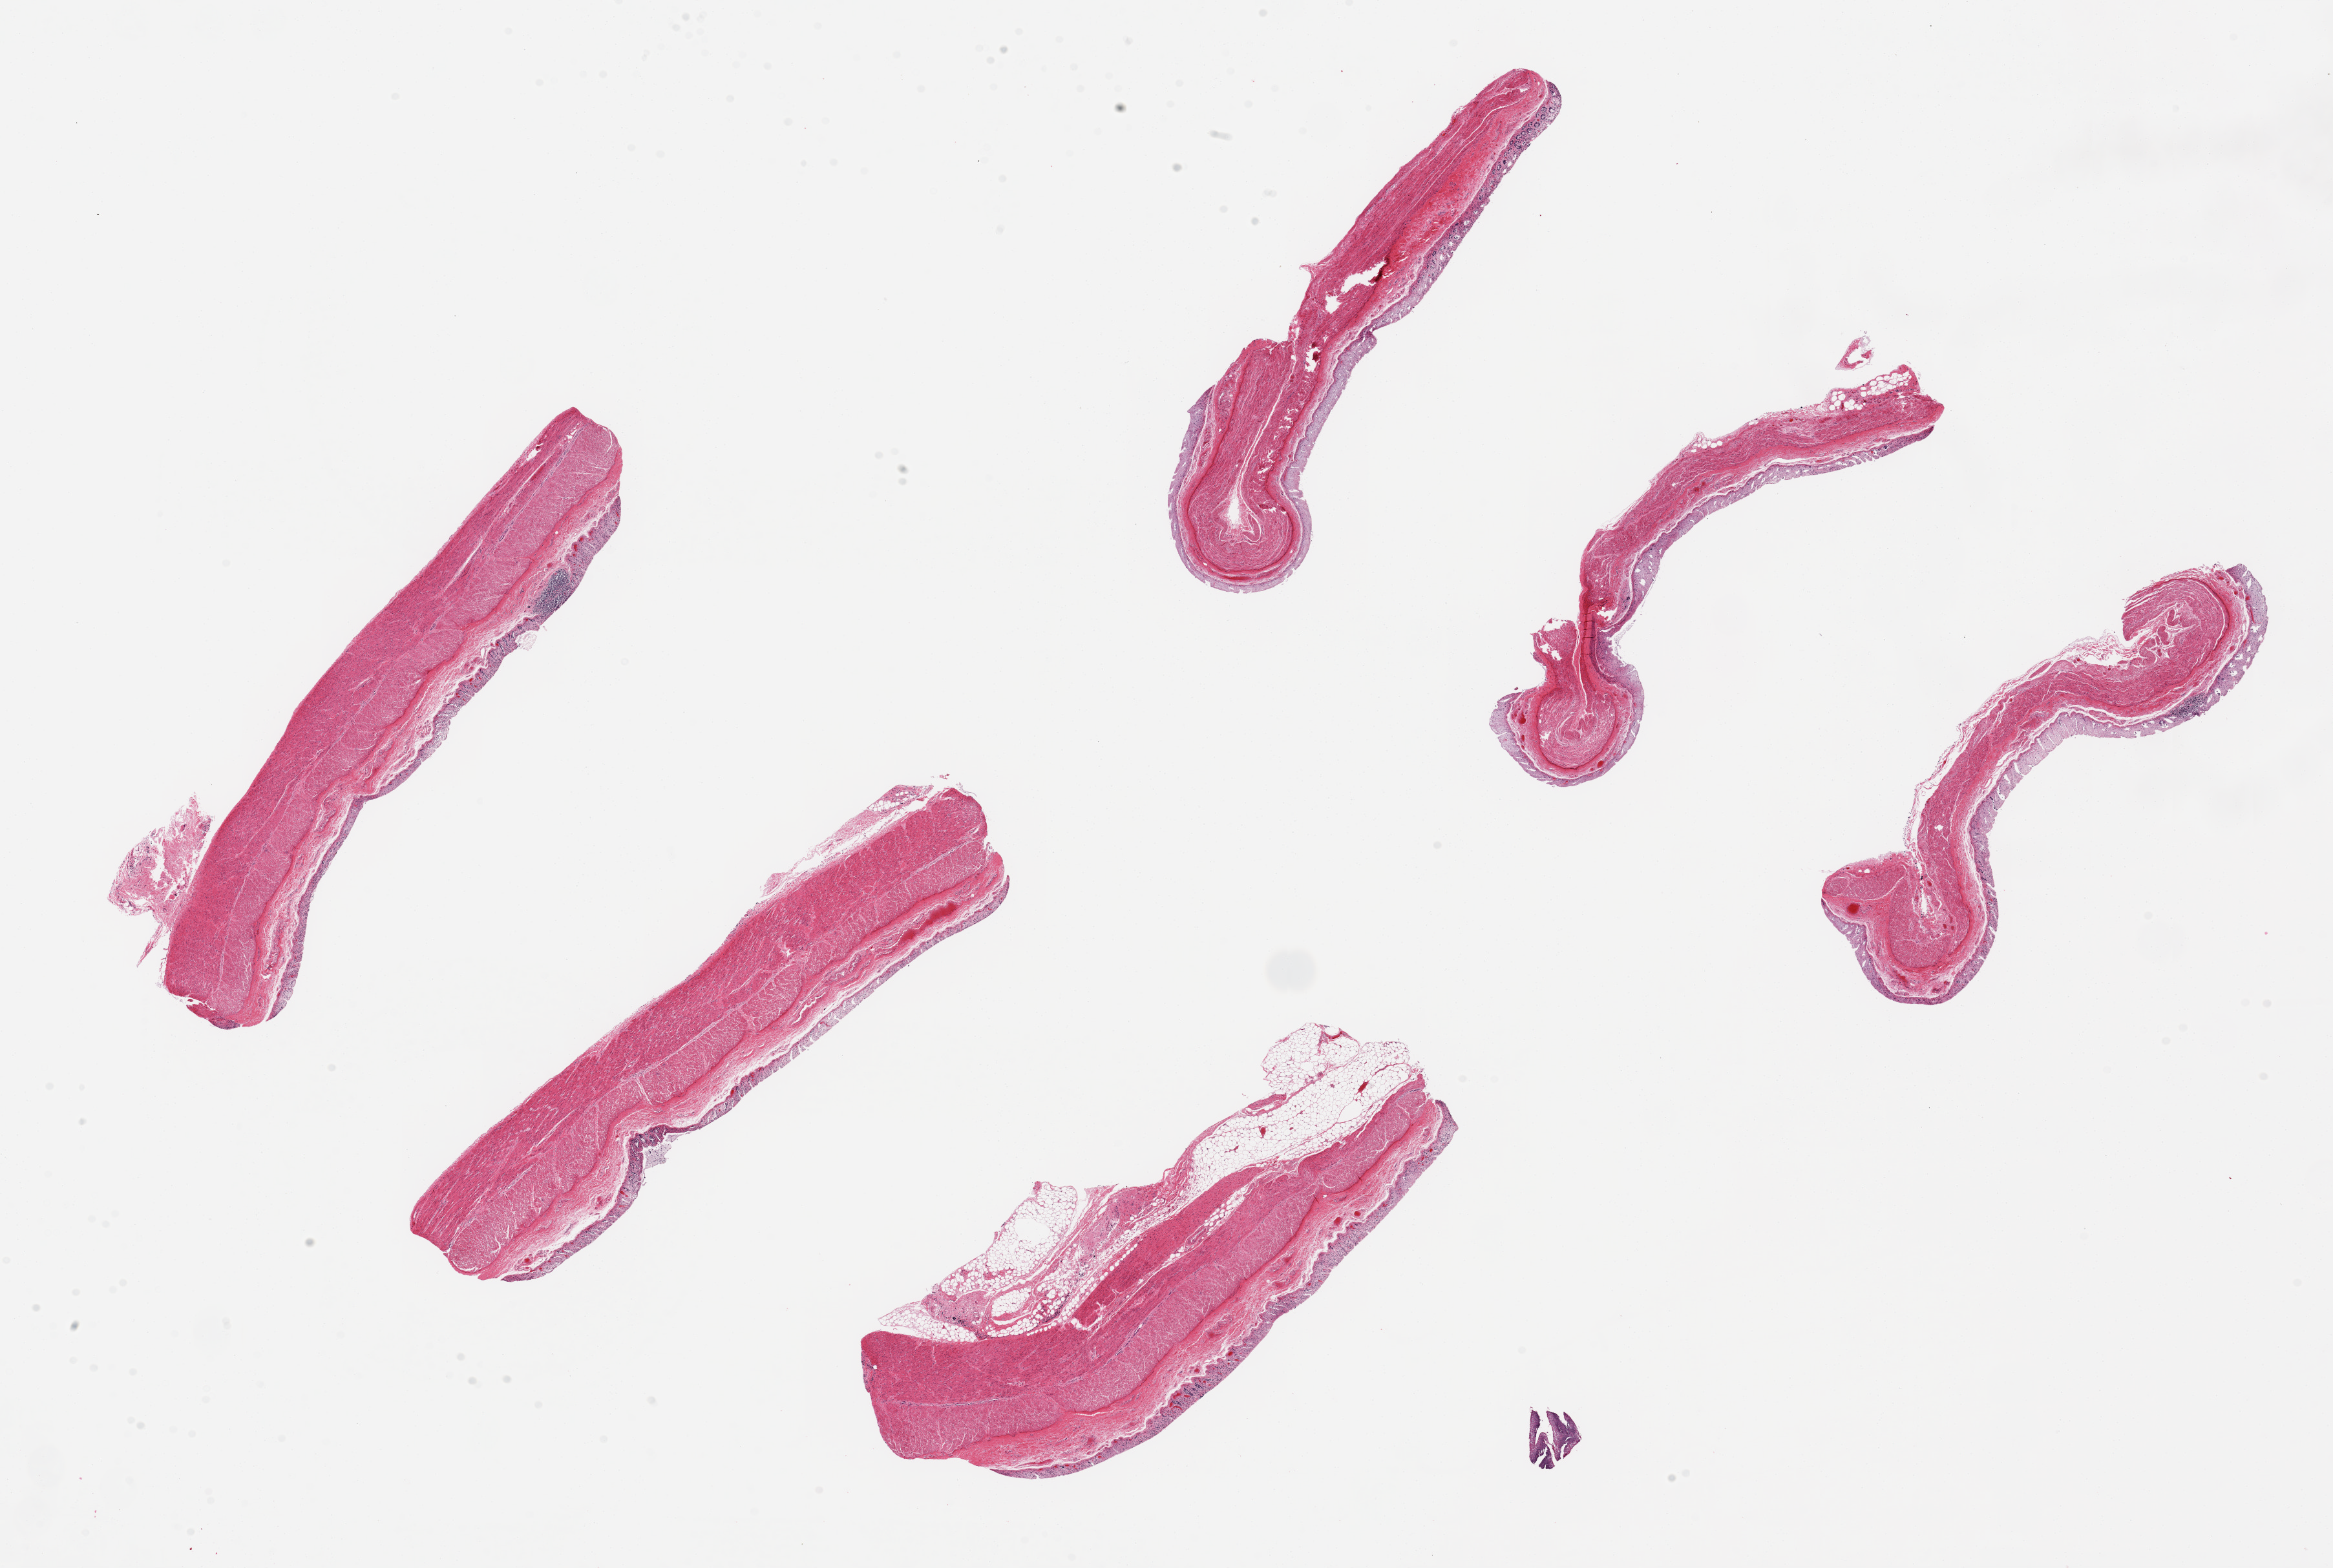
Digitized H&E-stained section, a low-resolution overview of the entire scanned area, about 28.5 x 19.2 mm (slide scanned at 20x), PAXgene-fixed, paraffin-embedded tissue, sampled site (target tissue): transverse colon, donor tissue sample.
Reviewer comment on this tissue sample: 6 pieces up to 8x3 mm; mucosa totally autolyzed; muscularis slightly autolyzed; 0.6 mm squamous floater.